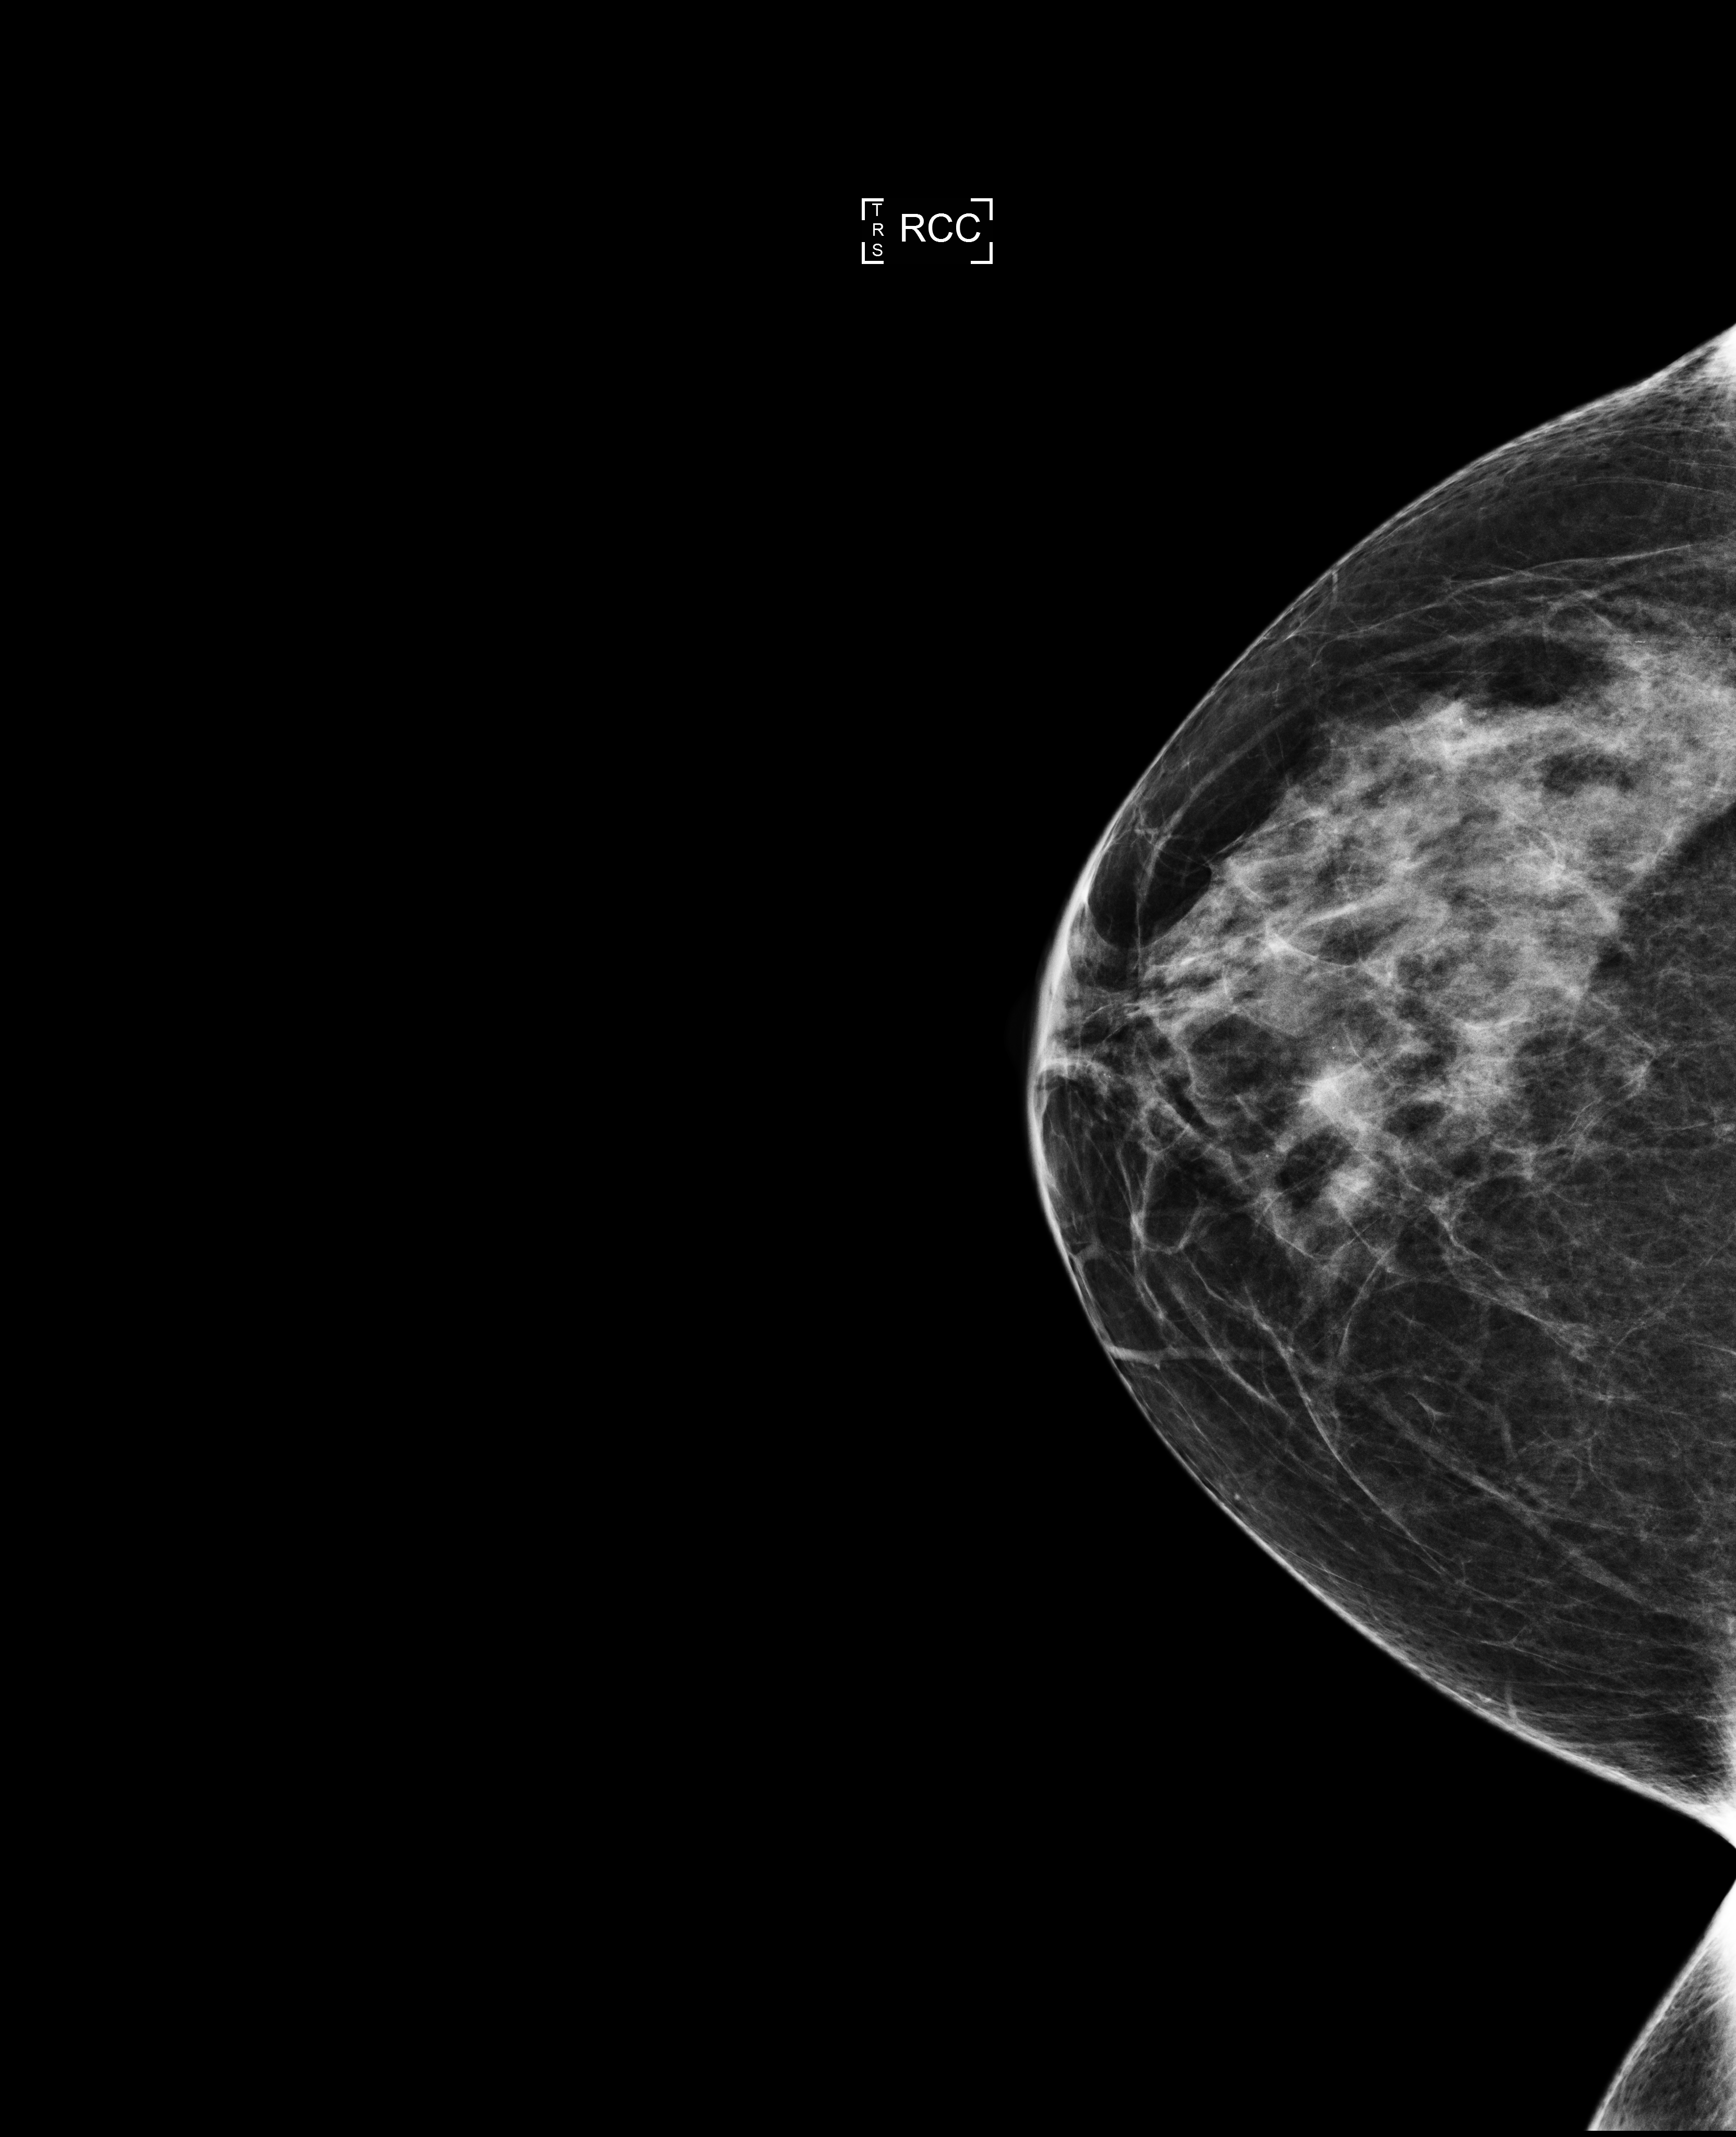
Screening examination; compressed breast thickness 56 mm. Patient aged 64 years (female).
Image type: full-field digital mammogram. Breast: right. Projection: craniocaudal (CC) view.